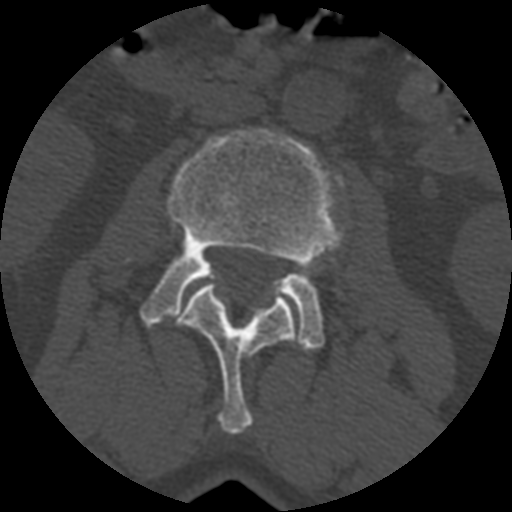
CT including the spine, one axial slice. Position 319 of 399 along the scan axis. Reconstruction kernel STANDARD. 120 kVp. Bone window (W 1800 / L 400 HU). 512 × 512 image matrix, field of view 160 × 160 mm. Patient age 71 years. From the clinical record (not read from this slice): primary cancer: prostate.
Outlined on this slice (semi-automatically segmented with operator editing):
- L2 vertebra: bounding box <173,283,295,436> (left, top, right, bottom; pixels)
- L3 vertebra: <140,130,344,350>